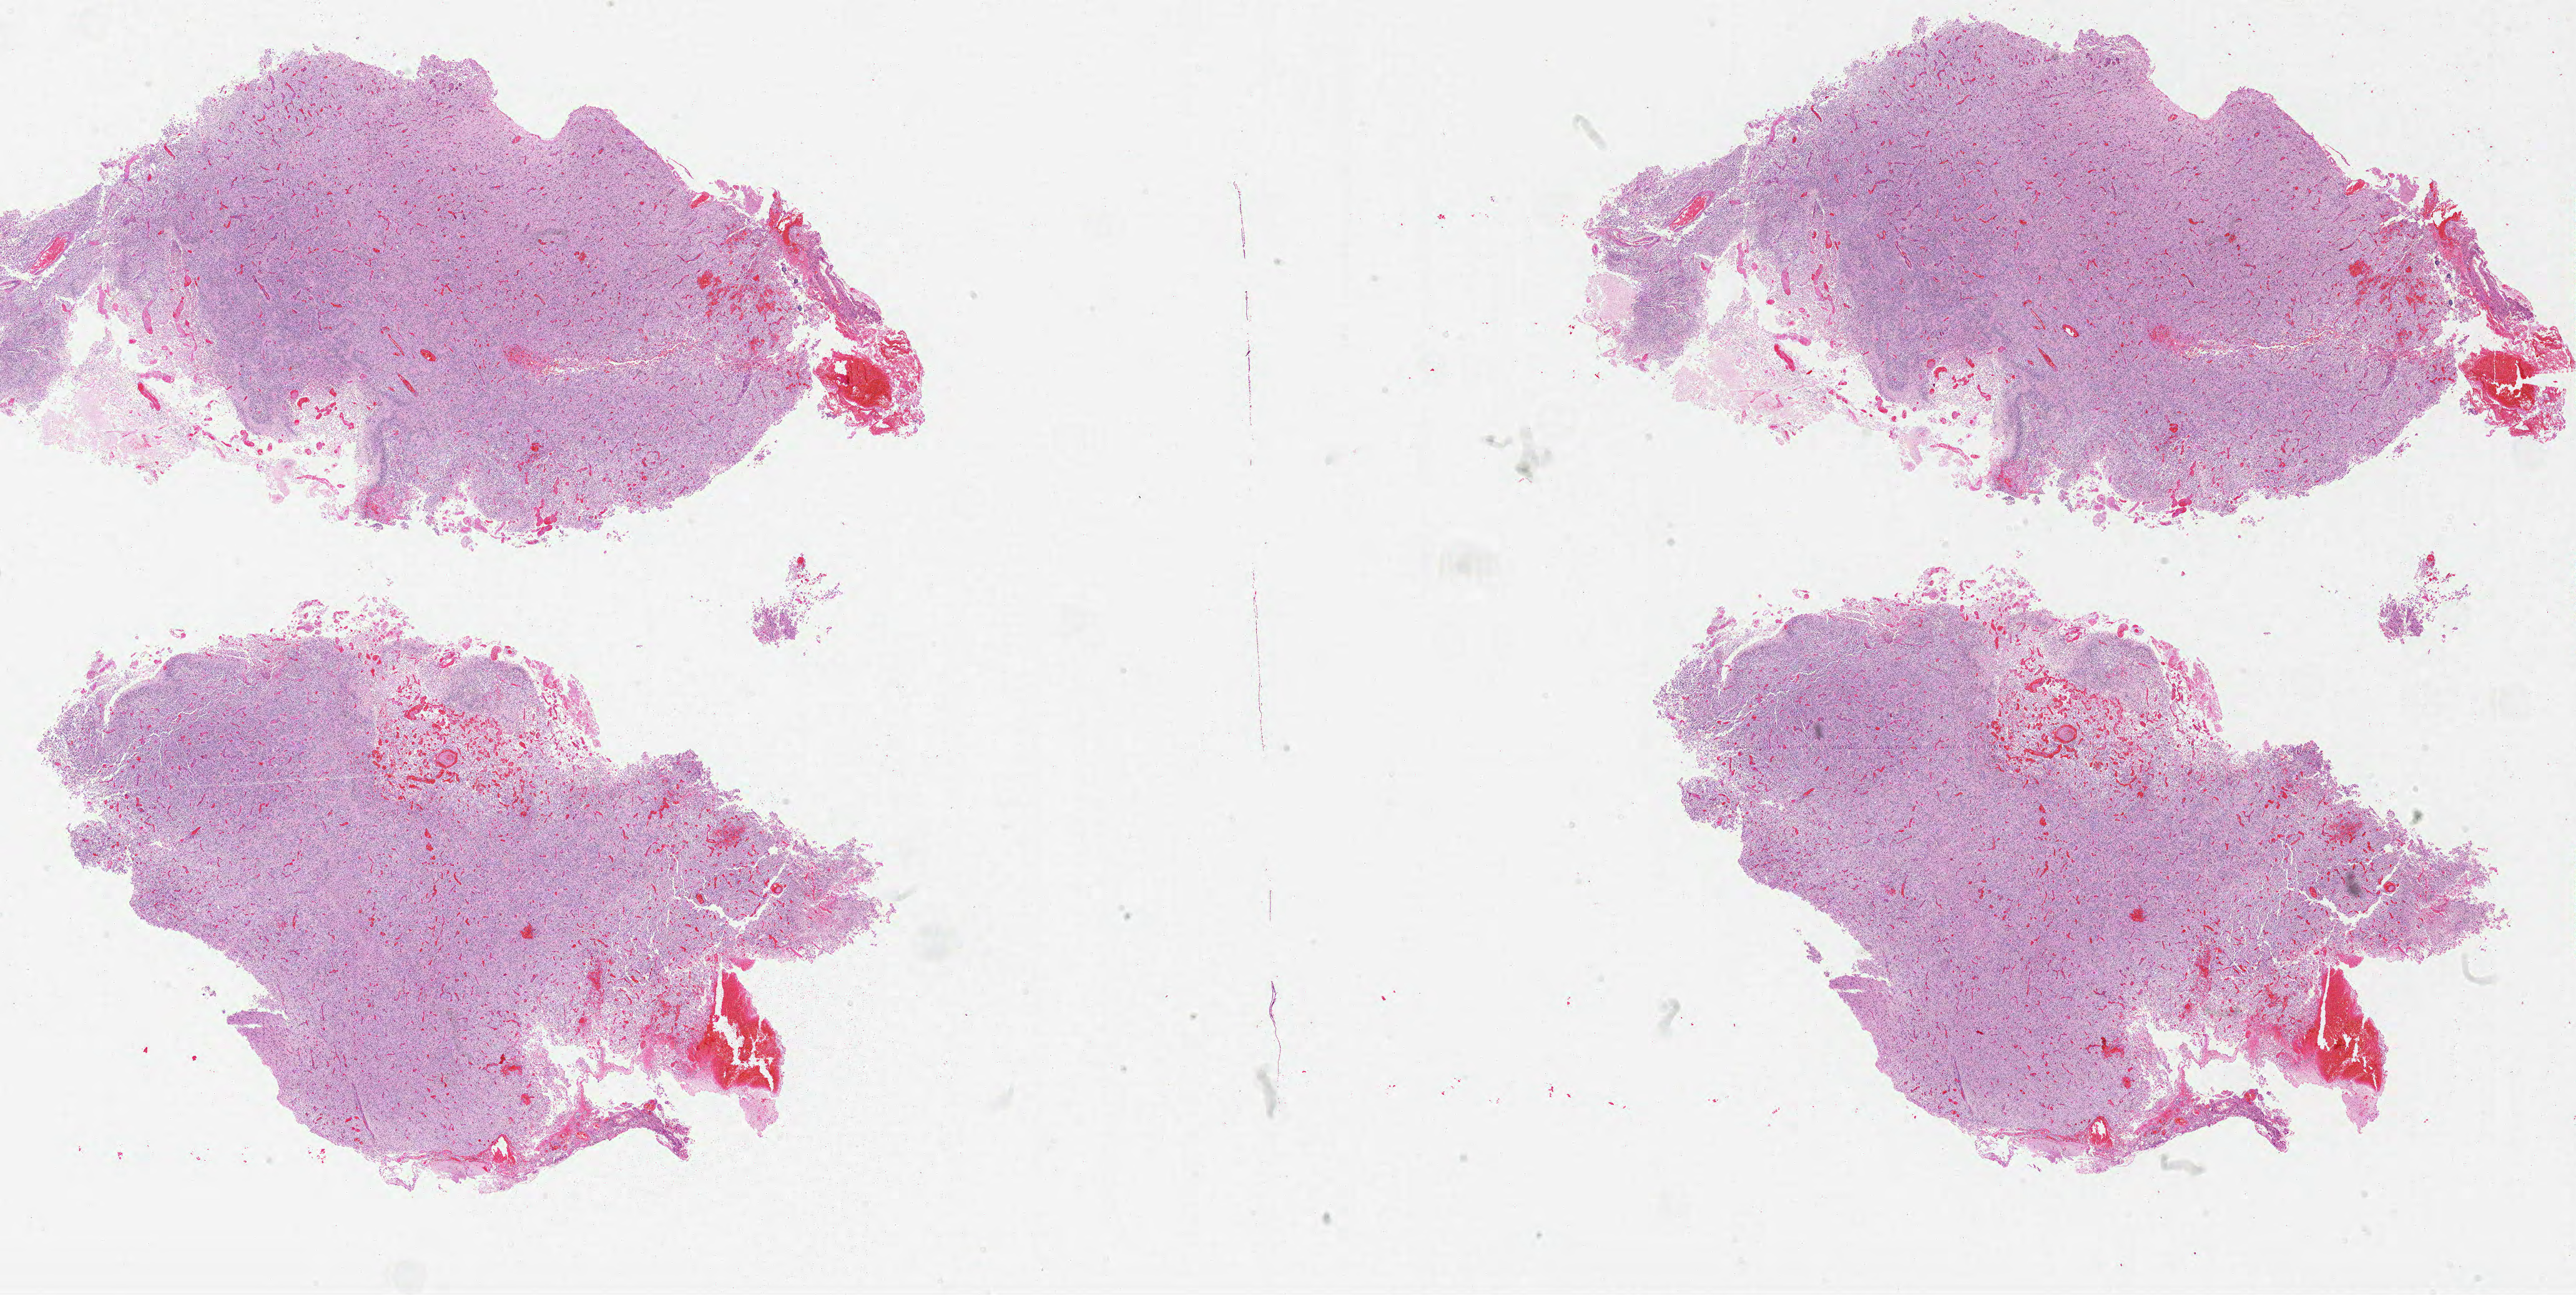
Whole-slide histology image, H&E — whole scanned area (about 33.0 x 16.6 mm, from a 20x scan) shown as a low-resolution overview; FFPE section; brain, primary tumour sample. Patient: male, age at initial diagnosis 46 years.
Histologic diagnosis: Glioblastoma.